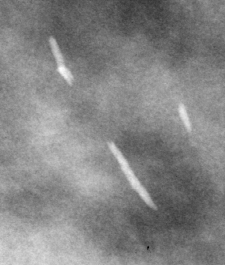
Cropped region of a digitized screen-film mammogram centred on a radiologist-marked abnormality; left breast; CC view.
Calcifications, morphology large rodlike / round and regular, distribution regional; BI-RADS assessment category 2; subtlety rating 5 on a 1 (subtle) to 5 (obvious) scale; benign without callback (not worked up further).